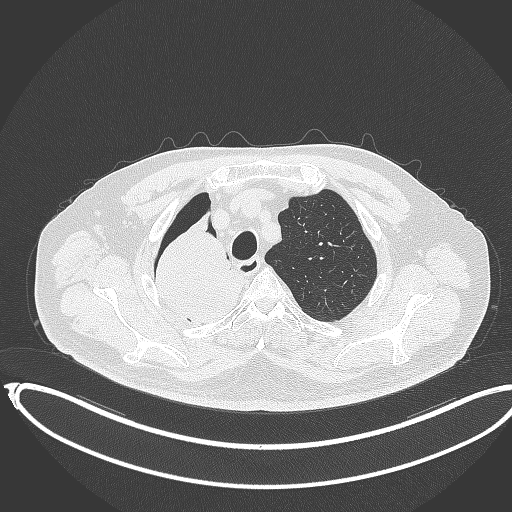
Chest CT, one axial slice; position 304 of 403 along the scan axis; 120 kVp; lung window (W 1500 / L -600 HU); 1 mm slice thickness; 512 × 512 image matrix. Patient: male, 68 years. Case-level facts recorded for this patient, not image findings: clinical TNM (as recorded): T2a N0 M0.
Outlined on this slice (rectangle marked by the reading radiologist):
- lung tumour (recorded histology: adenocarcinoma): bounding box <144,196,246,334> (left, top, right, bottom; pixels)